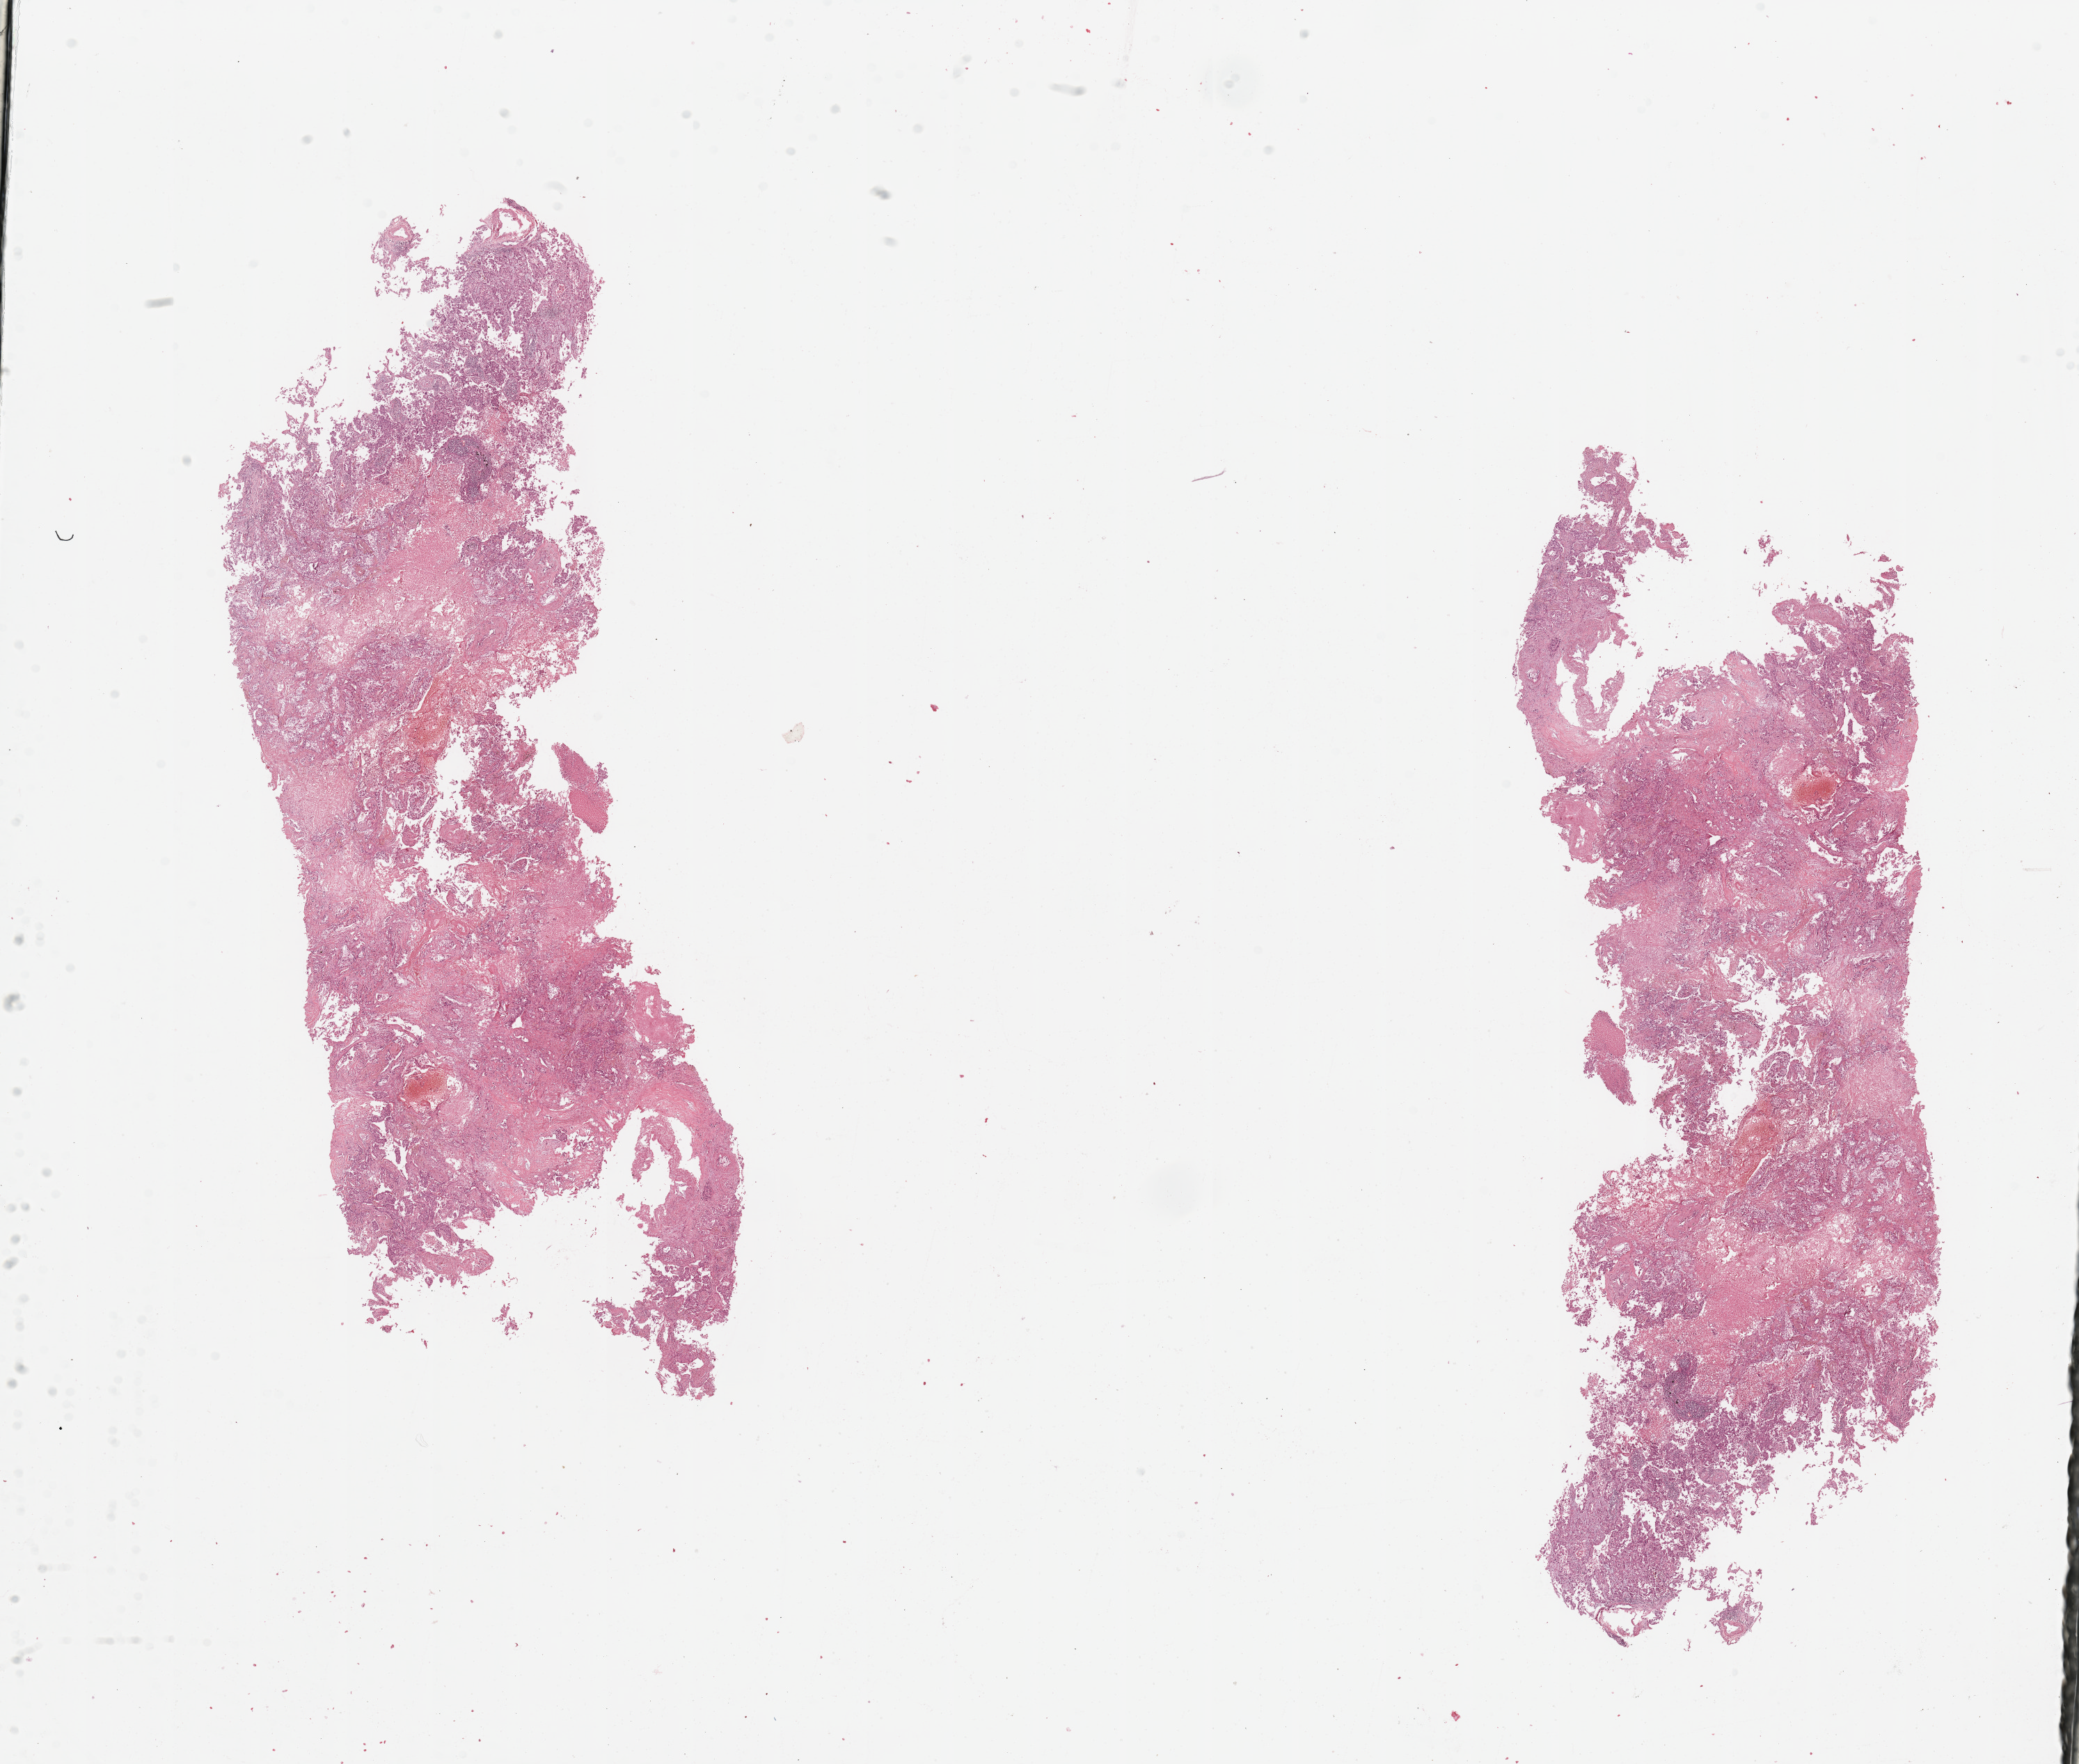
Digitized Hematoxylin and eosin (H&E) stained tissue section (whole slide) — whole scanned area (about 23.6 x 20.0 mm) shown as a low-resolution overview, lung, tumour tissue. Male, 72 y/o. Histologic grade: G2 (moderately differentiated).
AJCC pathologic stage: IB. Primary tumour site (as recorded): left lower lobe. Histologic diagnosis: Adenocarcinoma, NOS.